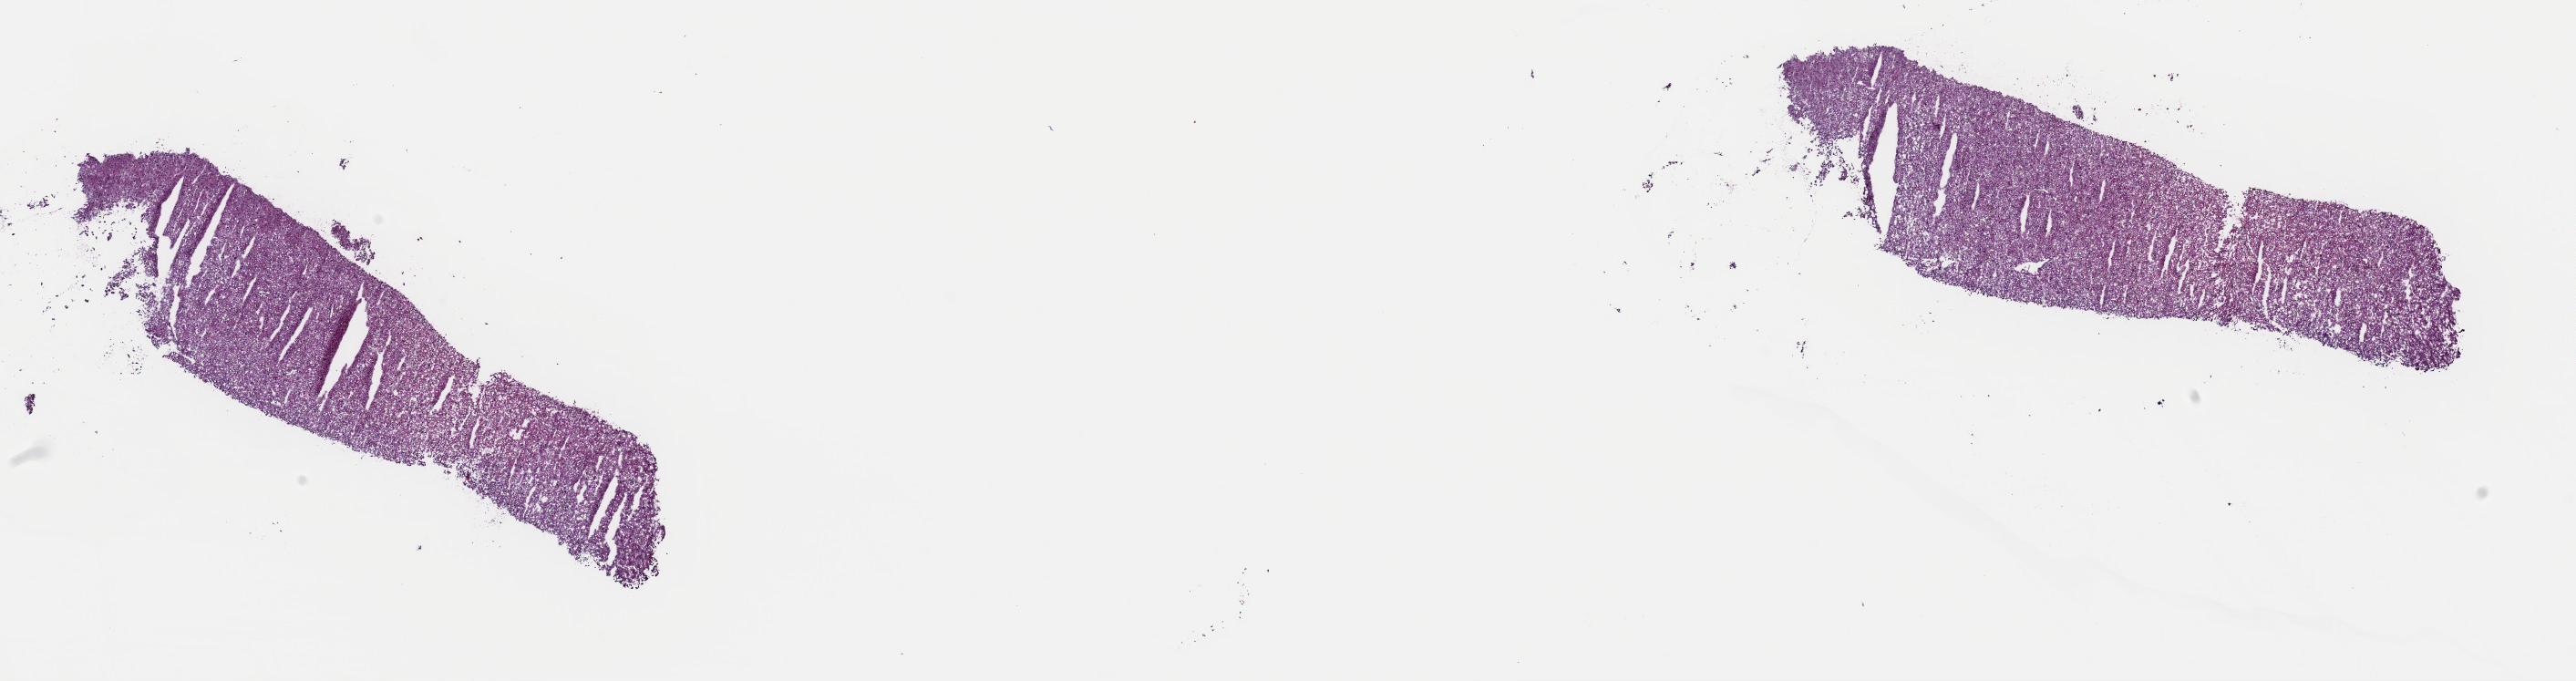
Whole-slide histology image, Hematoxylin and eosin (H&E) stained, shown as a low-resolution overview of the whole scanned area (about 22.3 x 5.9 mm), frozen section from the top of the tissue portion, primary tumour sample from the adrenal cortex. Male patient; age at initial diagnosis 45 years. Slide review estimates, as recorded: tumour cells 85%, tumour nuclei 85%, normal cells 0%, stromal cells 15%, necrosis 0%. Infiltration values recorded for this section: lymphocyte infiltration 0%, monocyte infiltration 0%, neutrophil infiltration 0%.
* laterality: left
* pathologic diagnosis: Adrenal cortical carcinoma (cortex of adrenal gland)